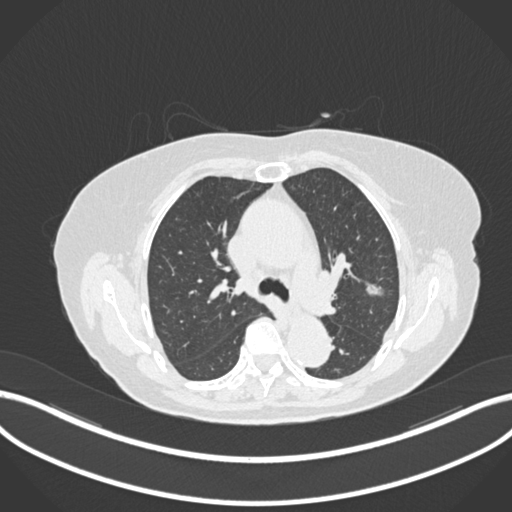
Chest CT, one axial slice; position 107 of 168 along the scan axis; 120 kVp; lung window (W 1500 / L -600 HU); 1 mm slice thickness; 512 × 512 image matrix. Female patient, age 75 years. Case-level facts recorded for this patient, not image findings: clinical TNM (as recorded): T1c N0 M0.
Outlined on this slice (rectangle marked by the reading radiologist):
- lung tumour (recorded histology: adenocarcinoma): bounding box (x1, y1, x2, y2) in pixels: (364, 279, 386, 301)